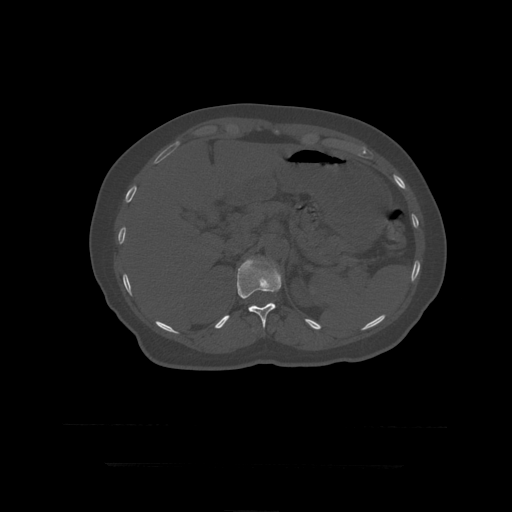
CT including the spine, one axial slice. Slice 194 of 399 in the series (ordered by position). Reconstruction kernel STANDARD. Bone window (W 1800 / L 400 HU). 1.25 mm slice thickness. 512 × 512 image matrix, field of view 450 × 450 mm. Patient age 41 years. From the clinical record (not read from this slice): primary cancer: breast.
Outlined on this slice (semi-automatic segmentation, software-assisted and operator-edited):
- L1 vertebra: bounding box <261,257,263,259> (left, top, right, bottom; pixels)
- T12 vertebra: <237,257,282,329>